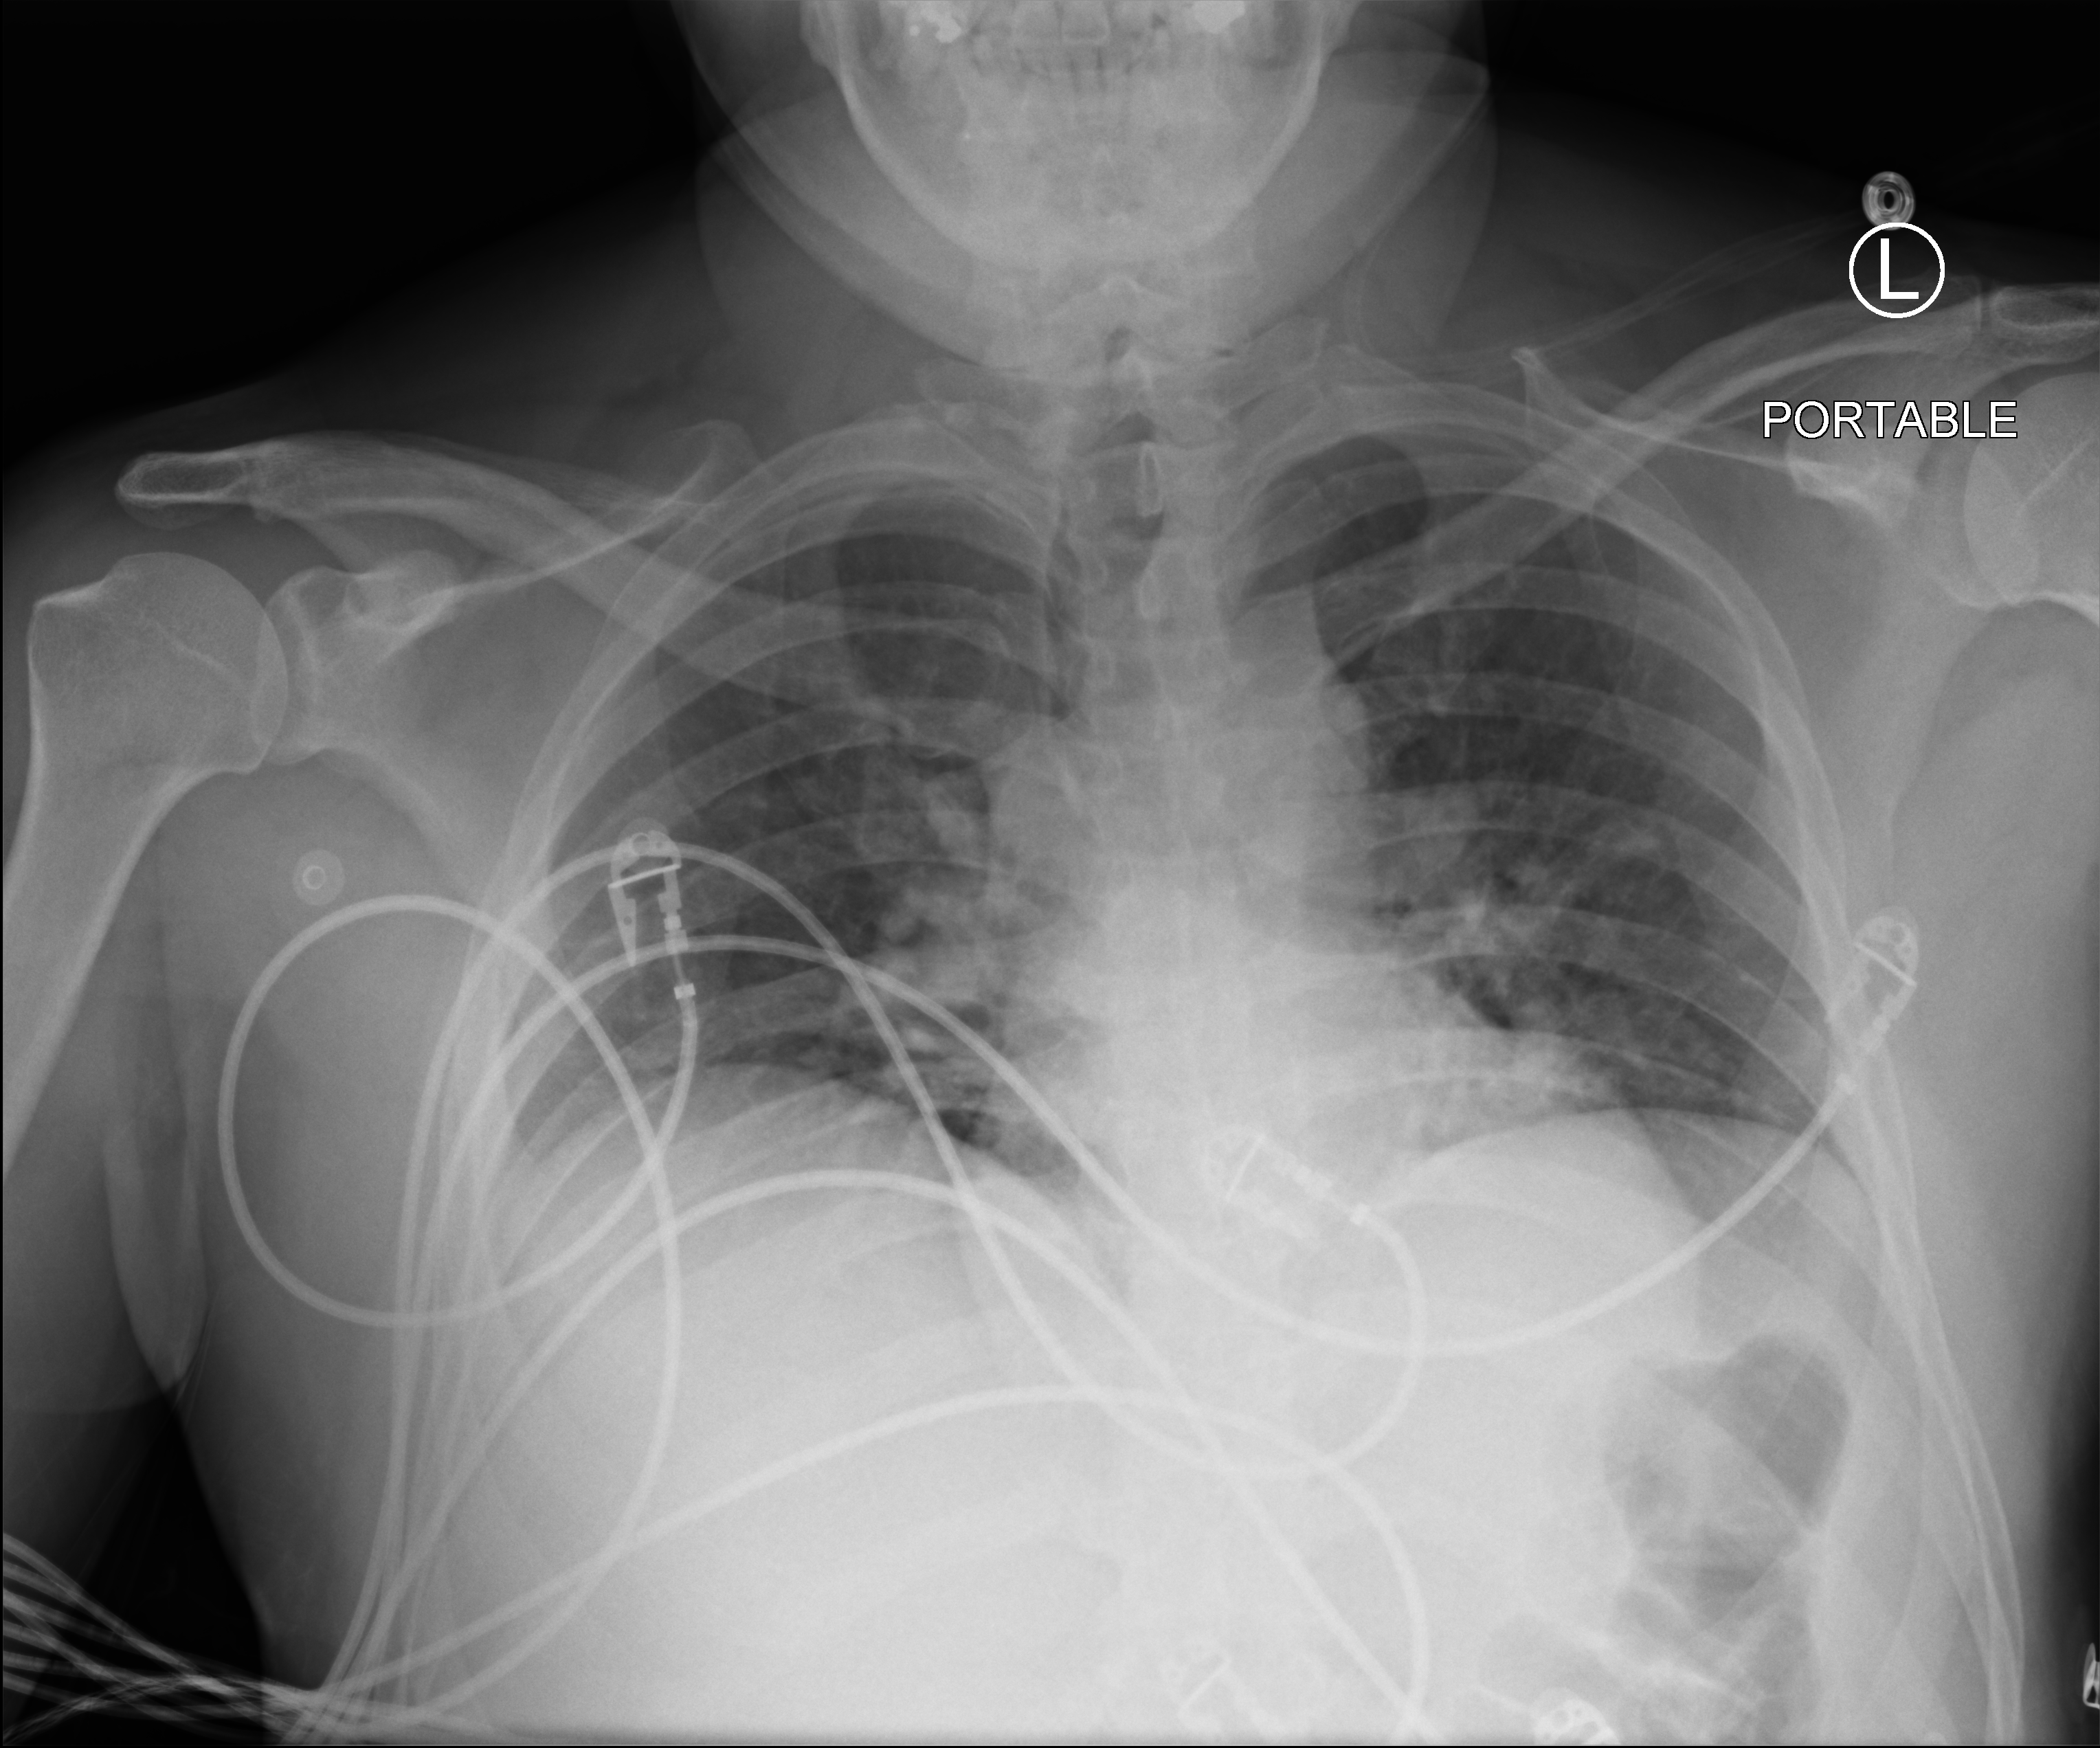
Chest X-ray (portable), anteroposterior (AP) projection. Adult patient hospitalised with COVID-19, age 18–59 years.
Hospital-stay facts (about this admission, not read from this image; timing relative to this image not recorded): other chronic lung disease (admission record): no; mechanically ventilated during this hospital stay: no.